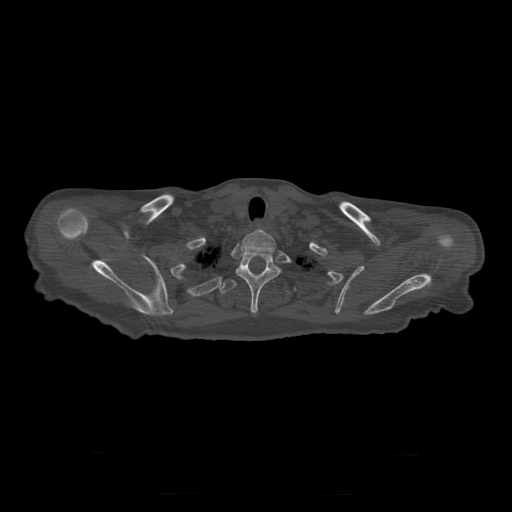
CT including the spine, one axial slice. Position 274 of 397 along the scan axis. Reconstruction kernel STANDARD. Bone window (W 1800 / L 400 HU). 512 × 512 image matrix. Patient age 73 years. Case-level facts recorded for this patient, not image findings: primary cancer: prostate.
Annotated regions visible in this slice (semi-automatically segmented with operator editing):
- T1 vertebra: bounding box [x1, y1, x2, y2] px = [243, 231, 276, 253]
- T2 vertebra: [236, 251, 281, 314]
- T3 vertebra: [220, 279, 289, 294]